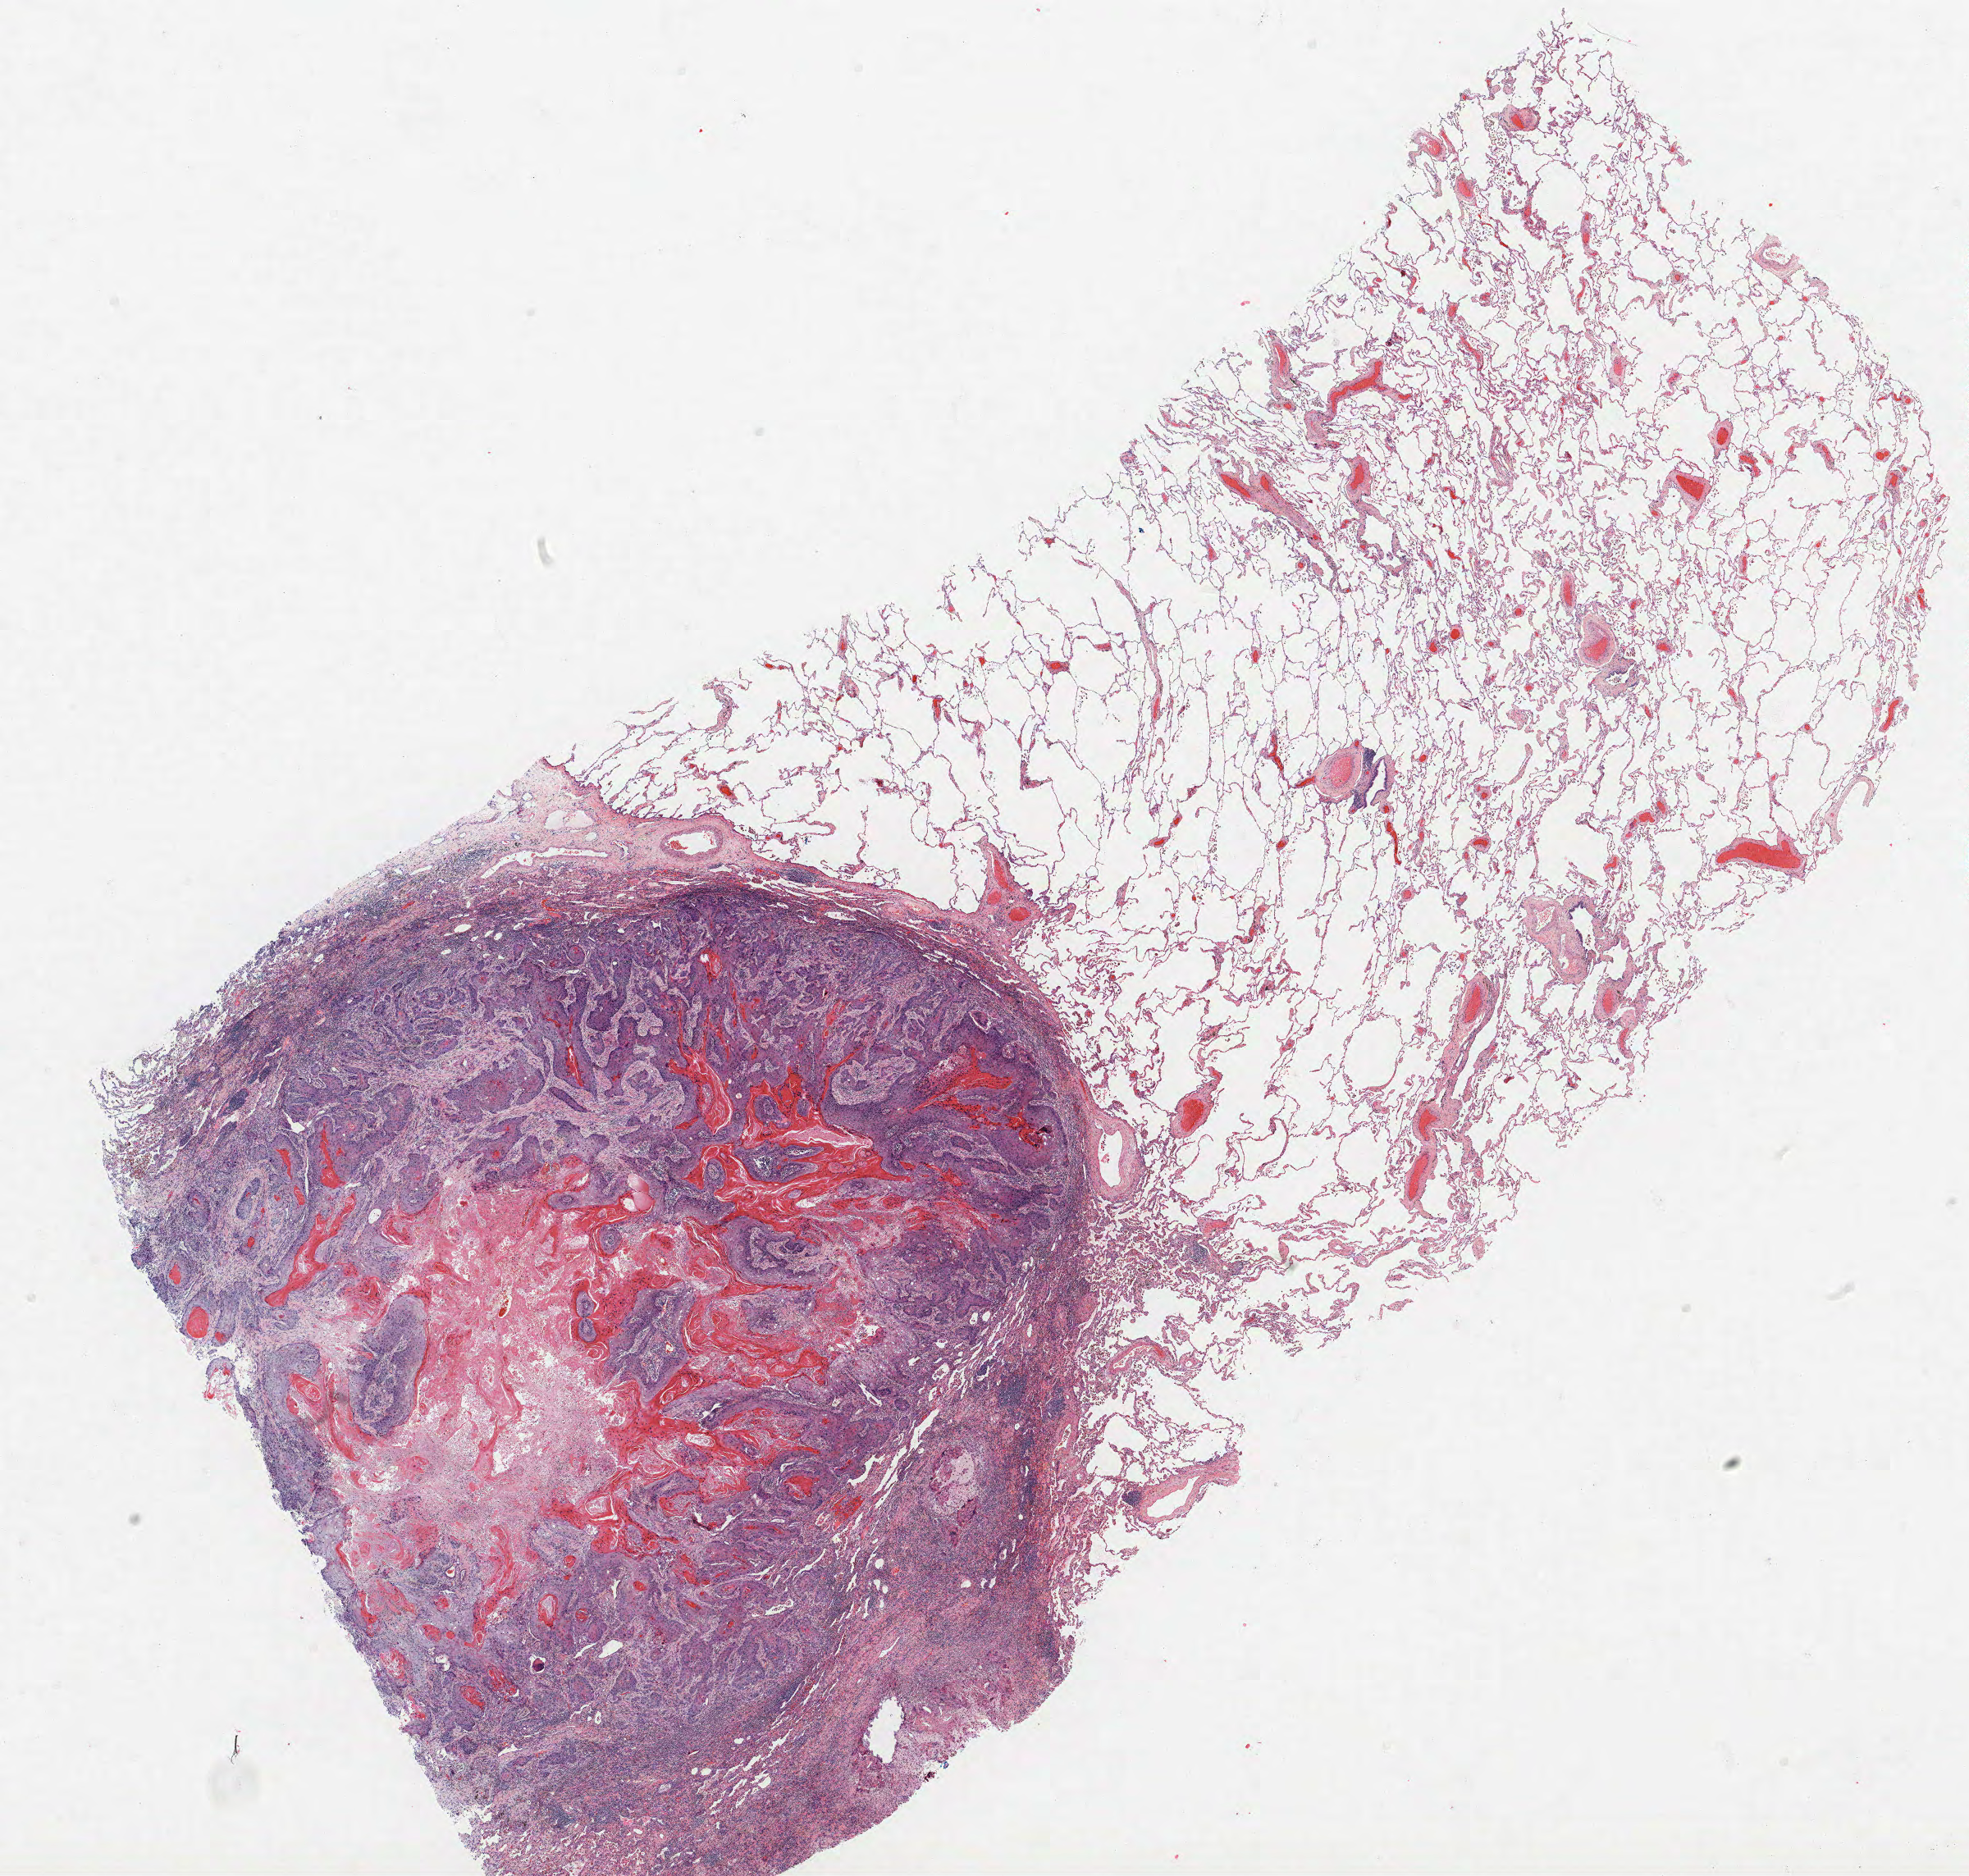
H&E-stained whole-slide image, low-resolution overview of the scanned area, about 19.2 x 18.3 mm (acquisition: 40x scan), FFPE section, lung. Male, age 57 at enrolment. Current smoker at enrolment. Grade: moderately differentiated (G2).
Primary tumour location (clinical record): left lower lobe. Stage (AJCC 6th edition): IB. Participant's lung-cancer diagnosis: Squamous cell carcinoma, NOS. Tumour size (pathology): 35 mm.